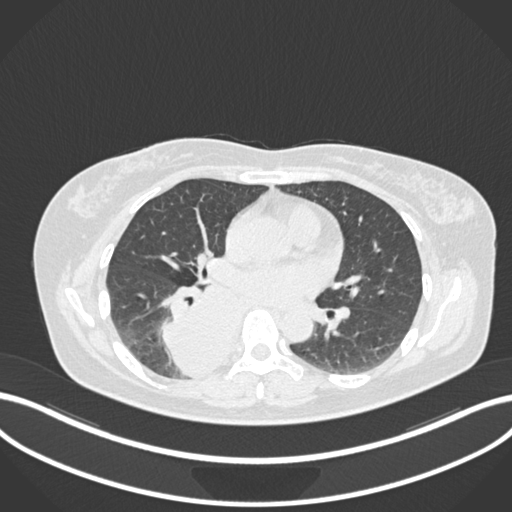
Chest CT, one axial slice. Position 585 of 677 along the scan axis. Reconstruction kernel B30f. Lung window (W 1500 / L -600 HU). 1 mm slice thickness. 512 × 512 image matrix, field of view 400 × 400 mm. Patient: female, 54 years. From the clinical record (not read from this slice): clinical TNM (as recorded): T4 N0 M0.
Structures marked on this image (bounding box drawn by a radiologist):
- lung tumour (recorded histology: adenocarcinoma): bounding box (x1, y1, x2, y2) in pixels: (150, 270, 243, 382)